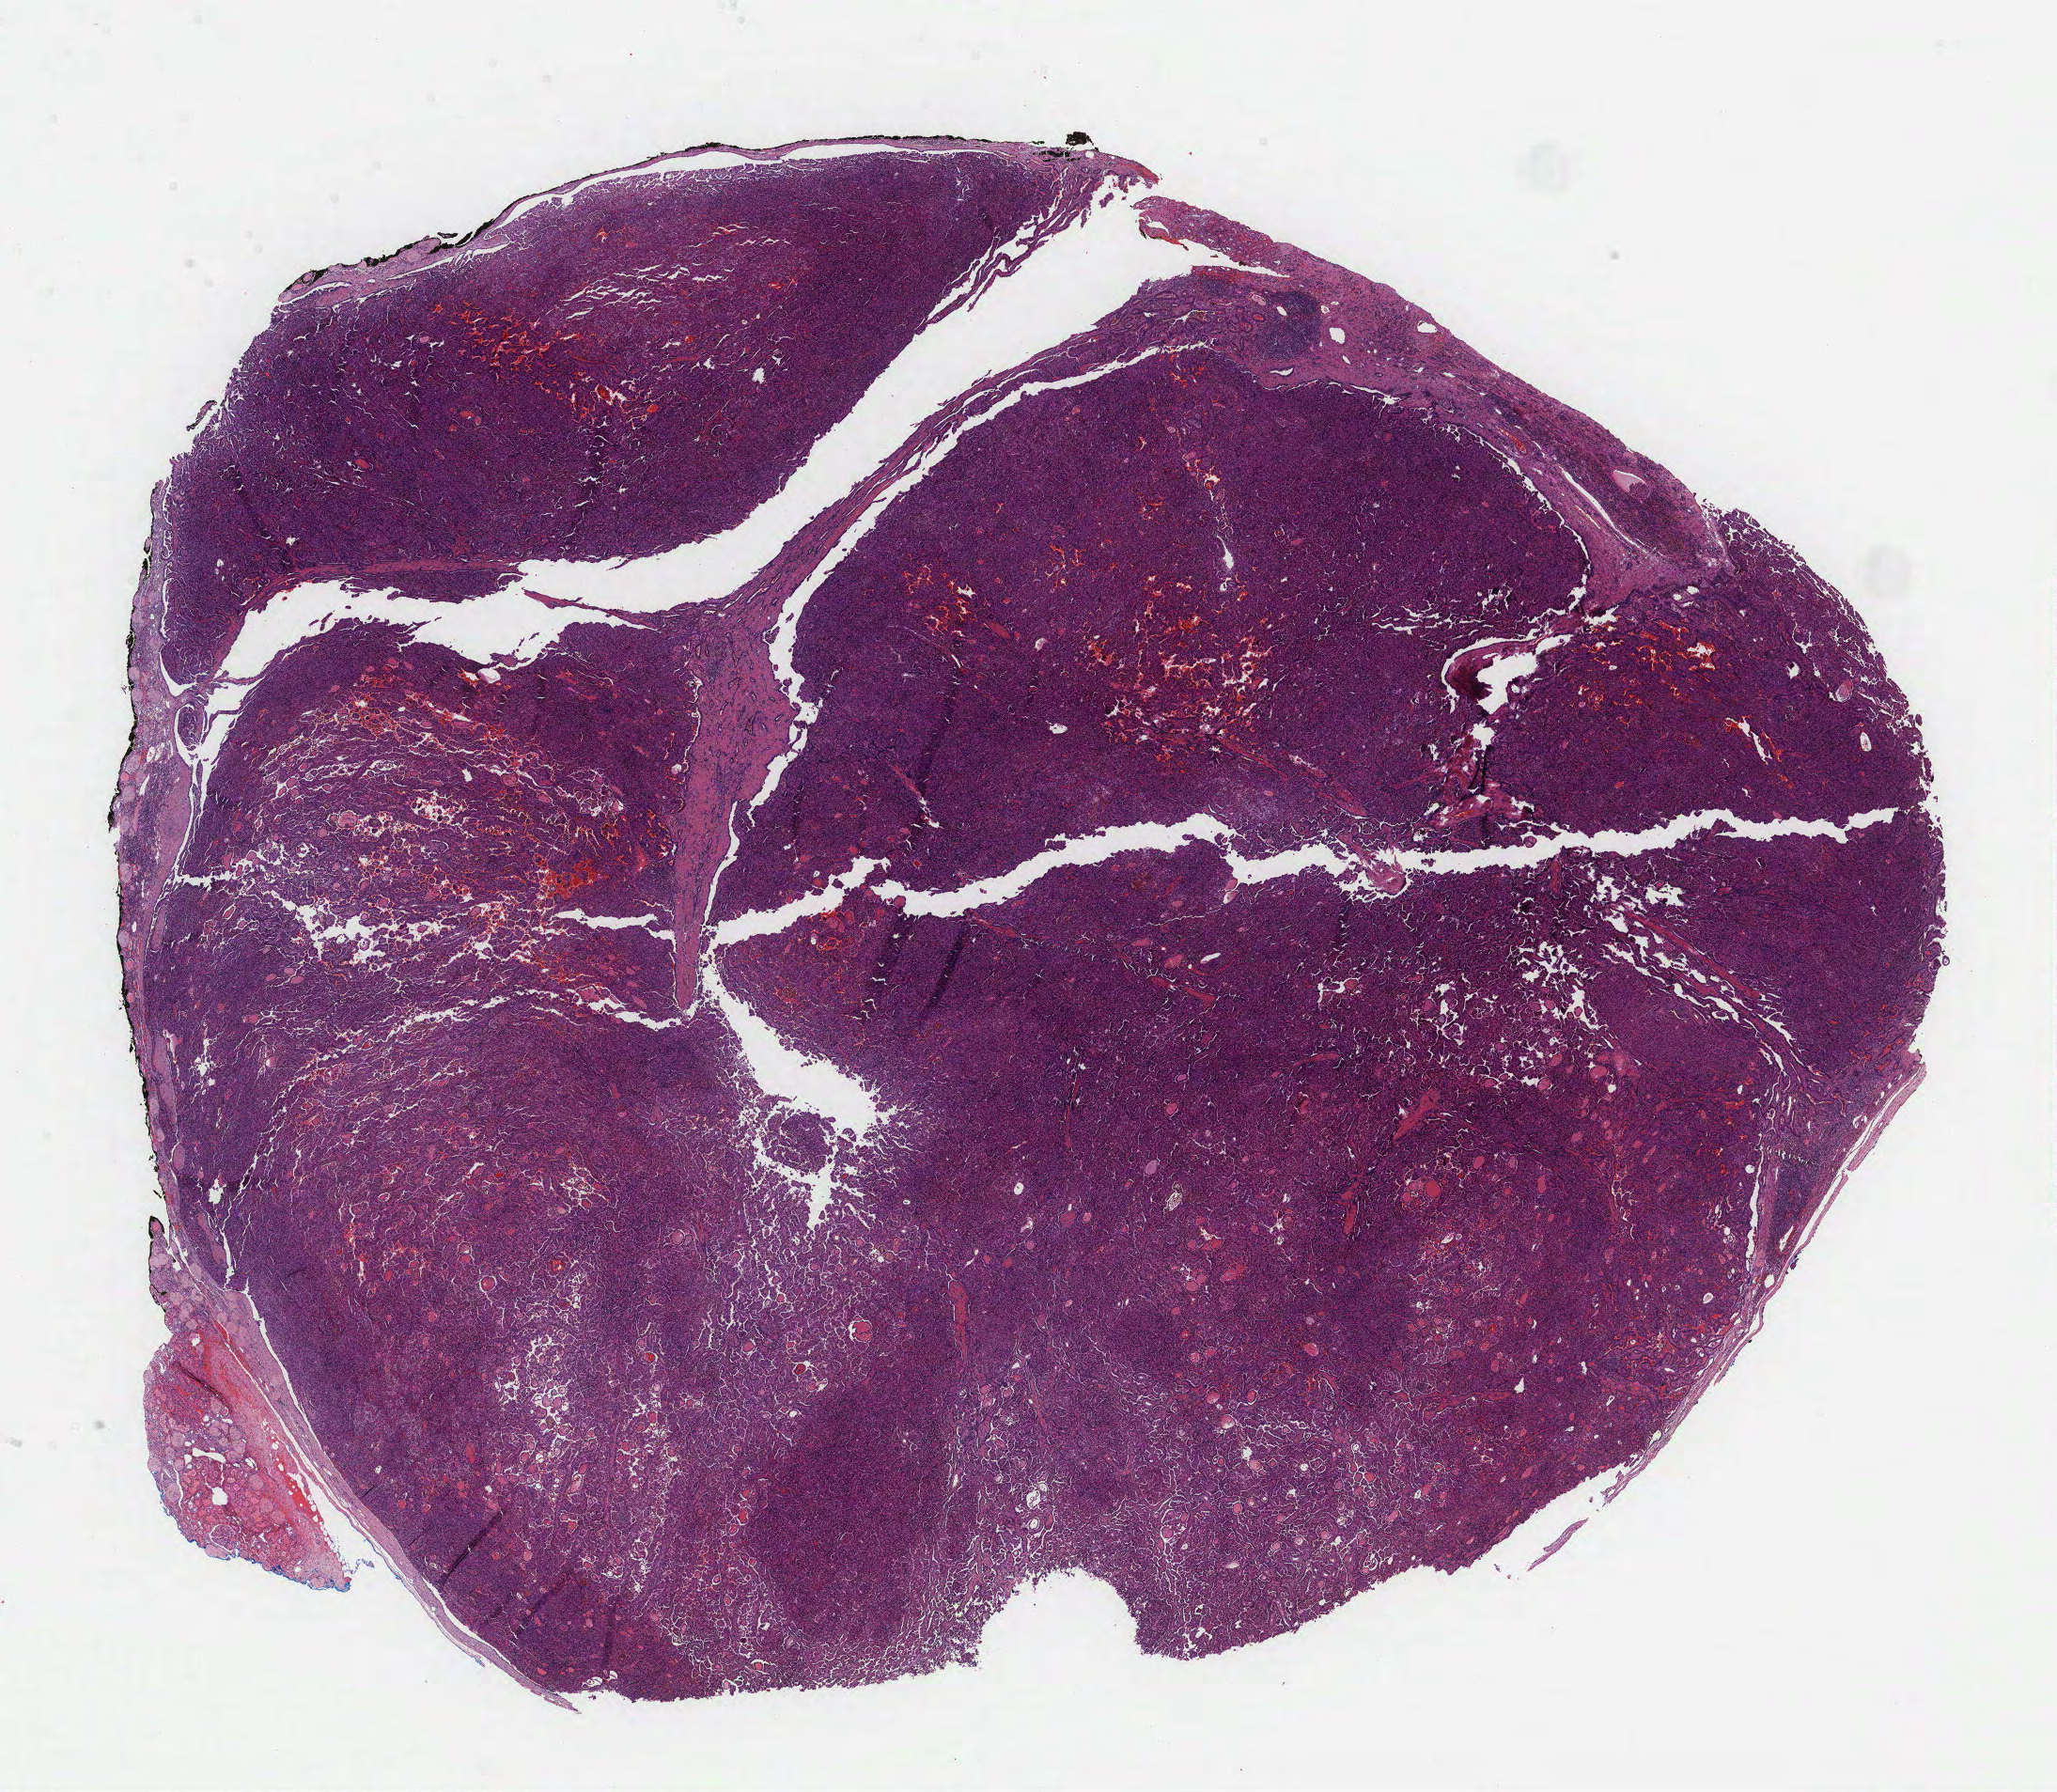
Digitized H&E-stained tissue section (whole slide) — shown as a low-resolution overview of the whole scanned area (about 17.7 x 15.4 mm), formalin-fixed paraffin-embedded (FFPE) diagnostic section, sample: primary tumour, kidney. Male patient; age at initial diagnosis 47 years.
Diagnosis: Papillary adenocarcinoma, NOS. Laterality: right. TNM: T1a NX MX. AJCC pathologic stage: I (7th edition).